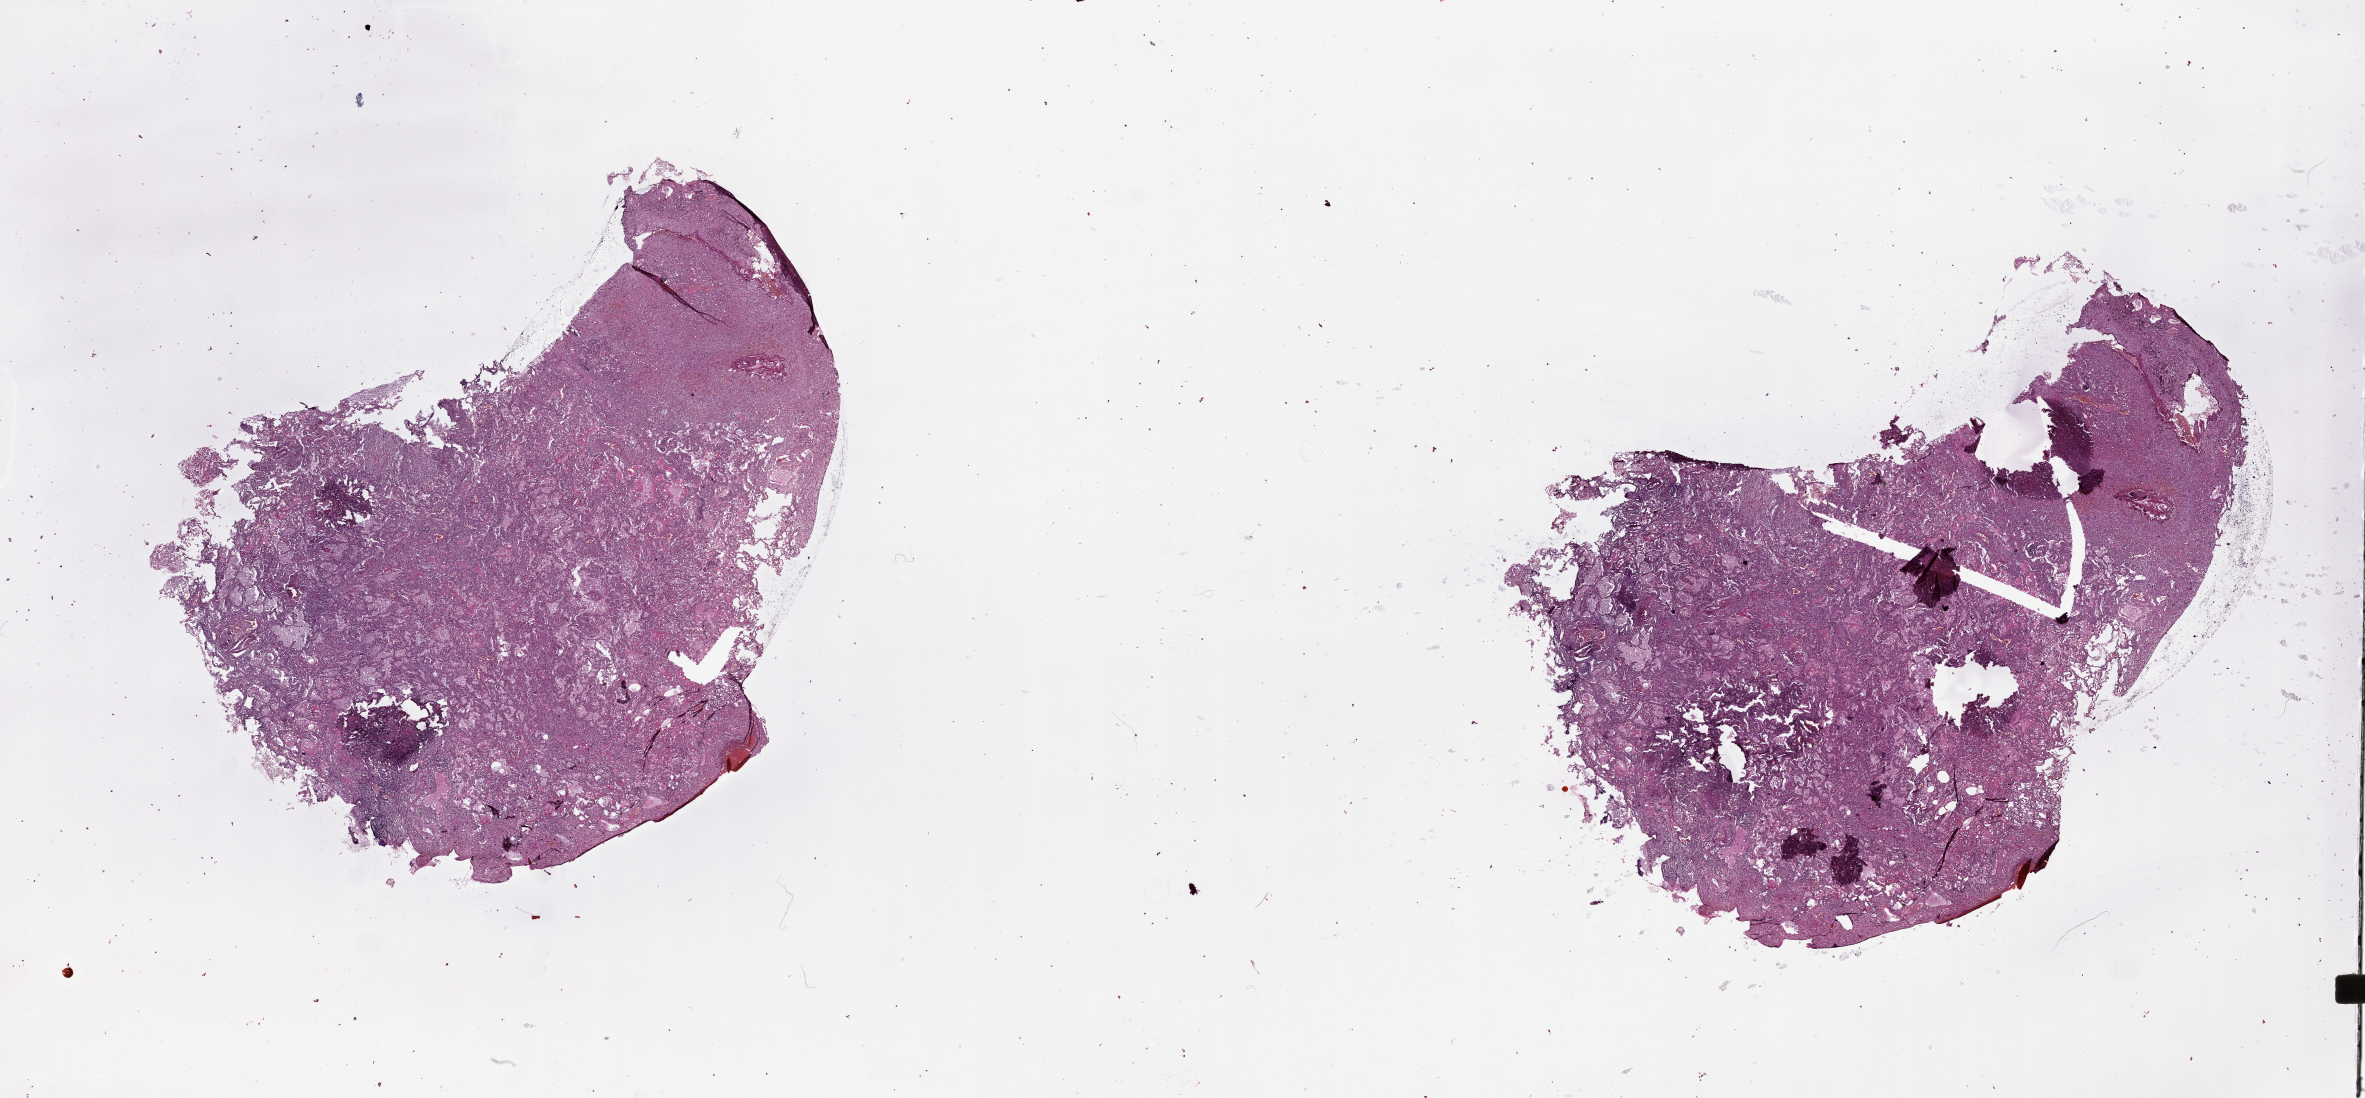
Whole-slide histology image, Hematoxylin and eosin (H&E) stained — a low-resolution overview of the entire scanned area, about 38.1 x 17.7 mm (from a 20x scan). Lung, normal (non-tumour) tissue. Male, 68 y/o.
This section: normal (non-tumour) tissue from the same patient. Patient diagnosis (cohort enrolment): squamous cell carcinoma (lung).